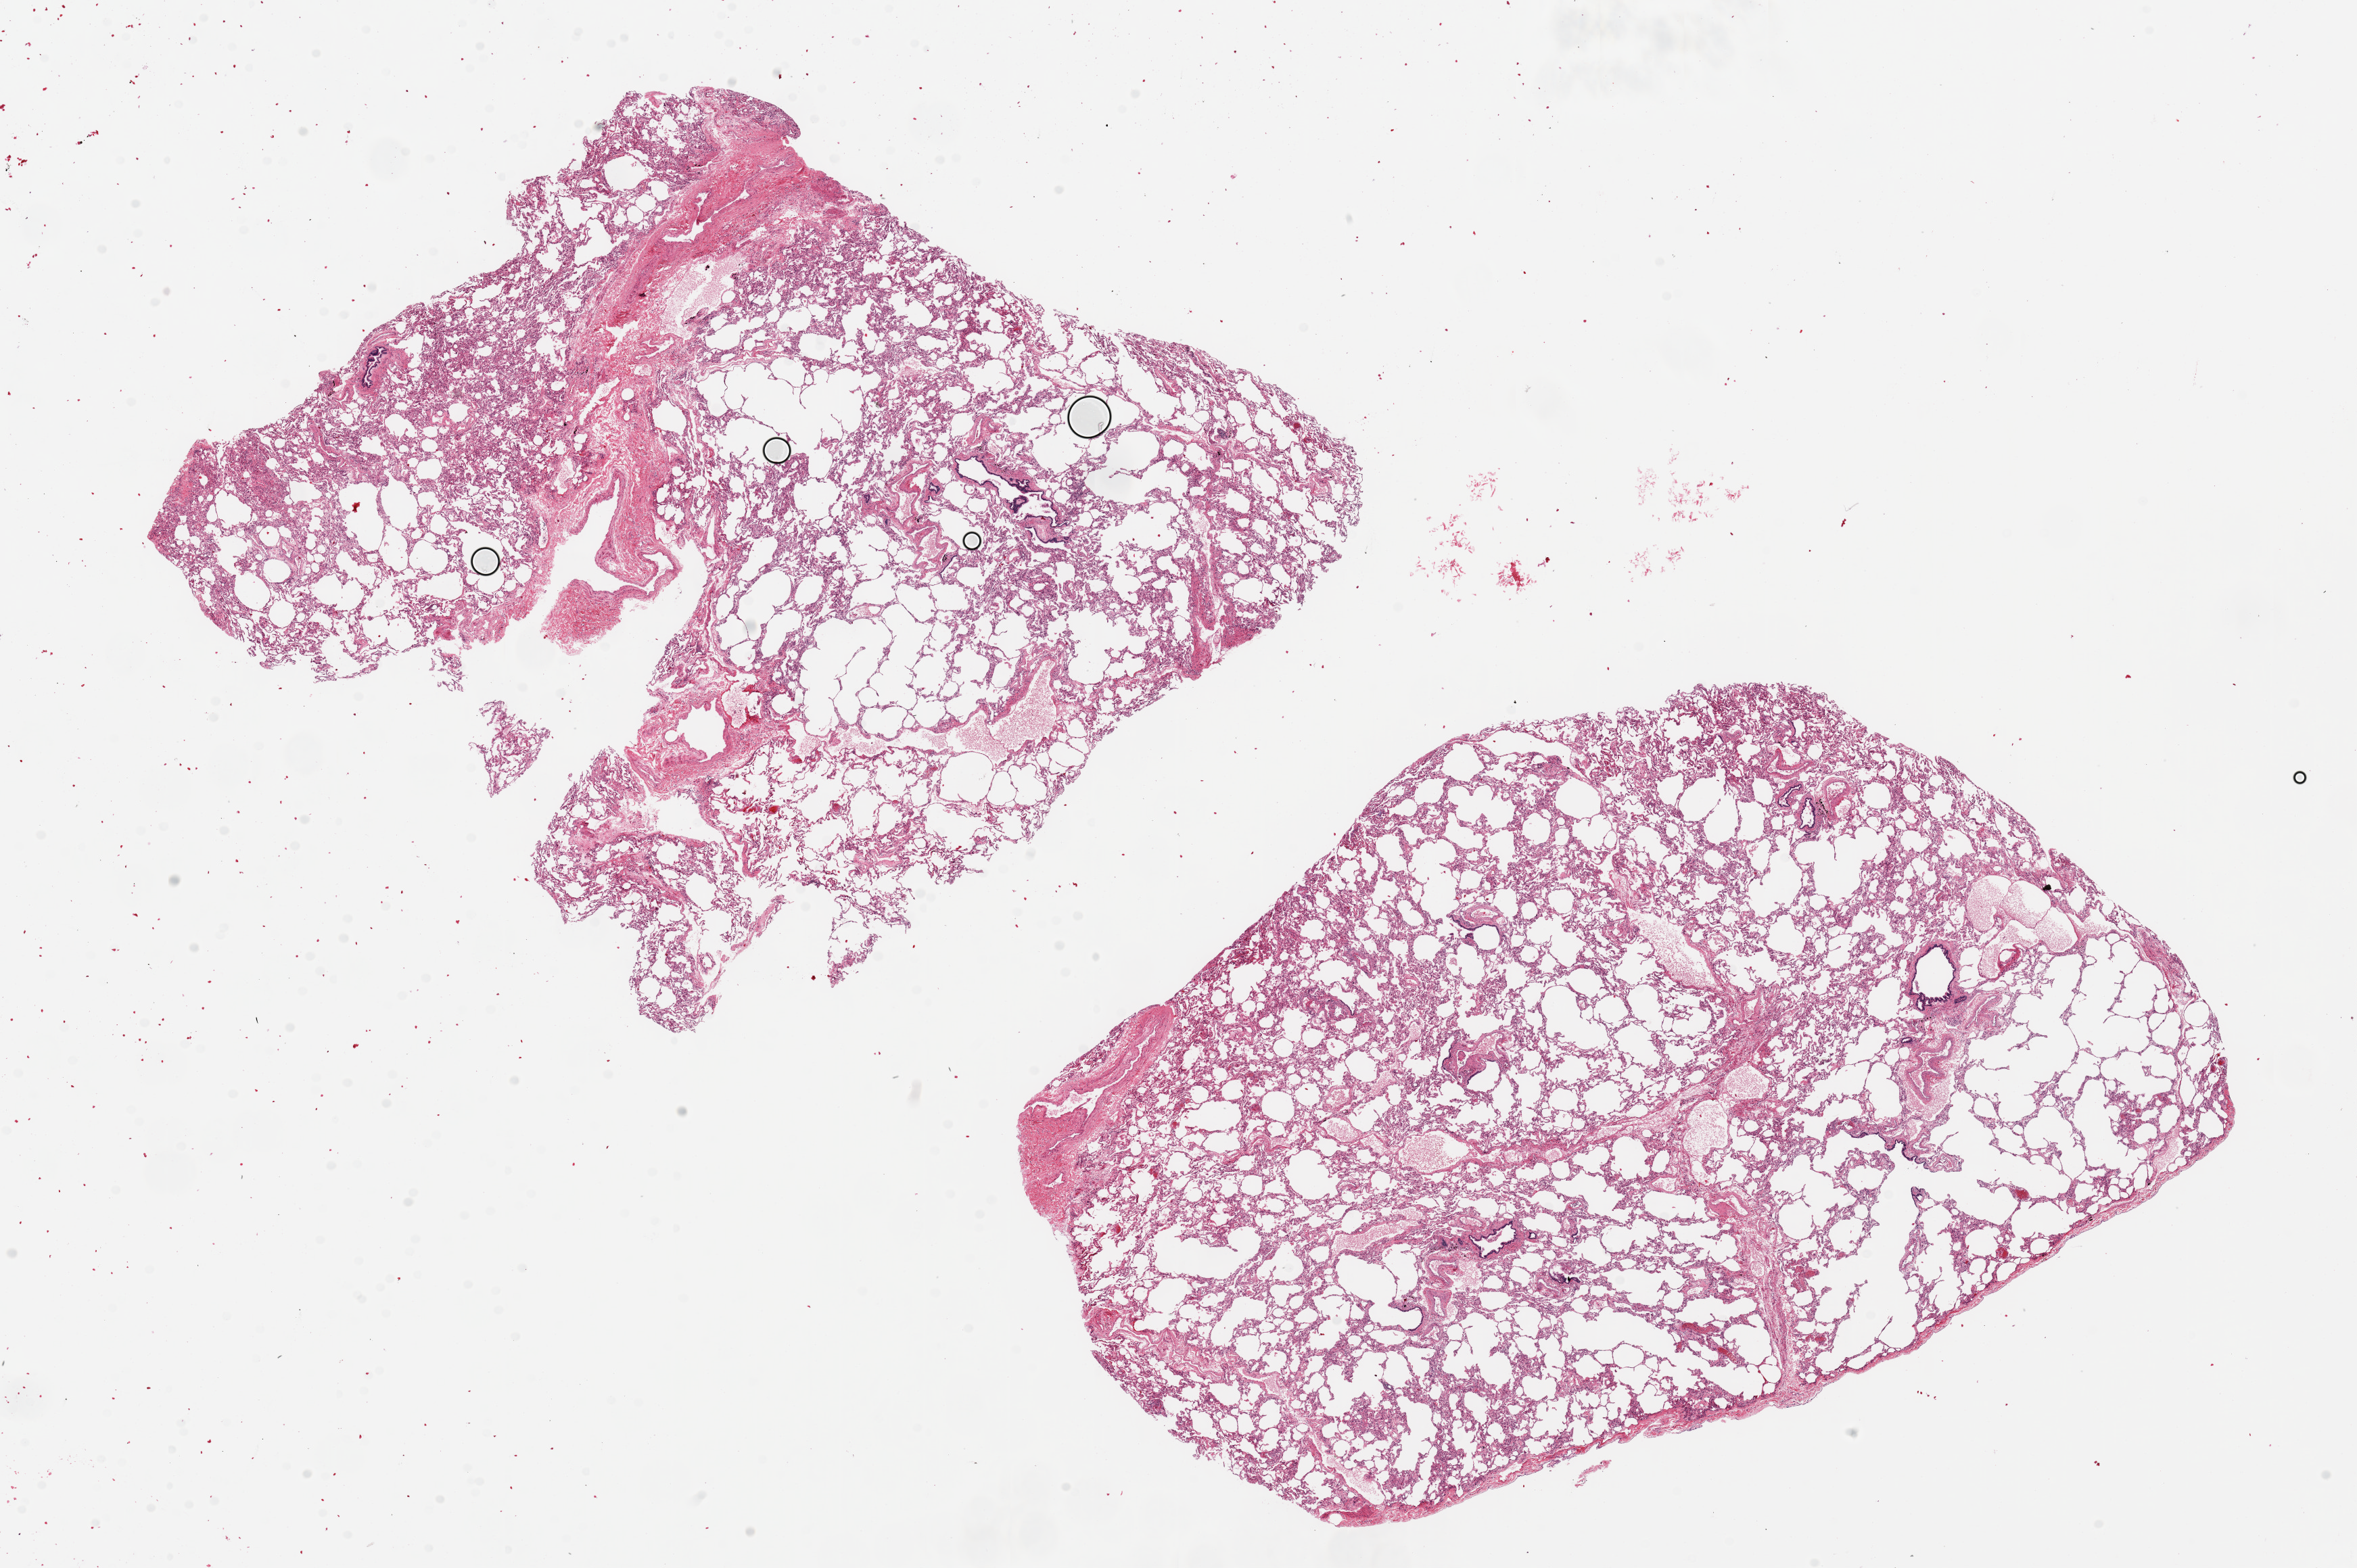
Digitized hematoxylin and eosin (H&E)-stained section, shown as a low-resolution overview of the whole scanned area (about 27.6 x 18.3 mm, from a 20x scan); PAXgene-fixed, paraffin-embedded tissue; target tissue: lung; tissue donor sample. Male donor.
* review note (as recorded): 2 pieces ~11x9mm. Minimal congestion; mild emphysematous changes